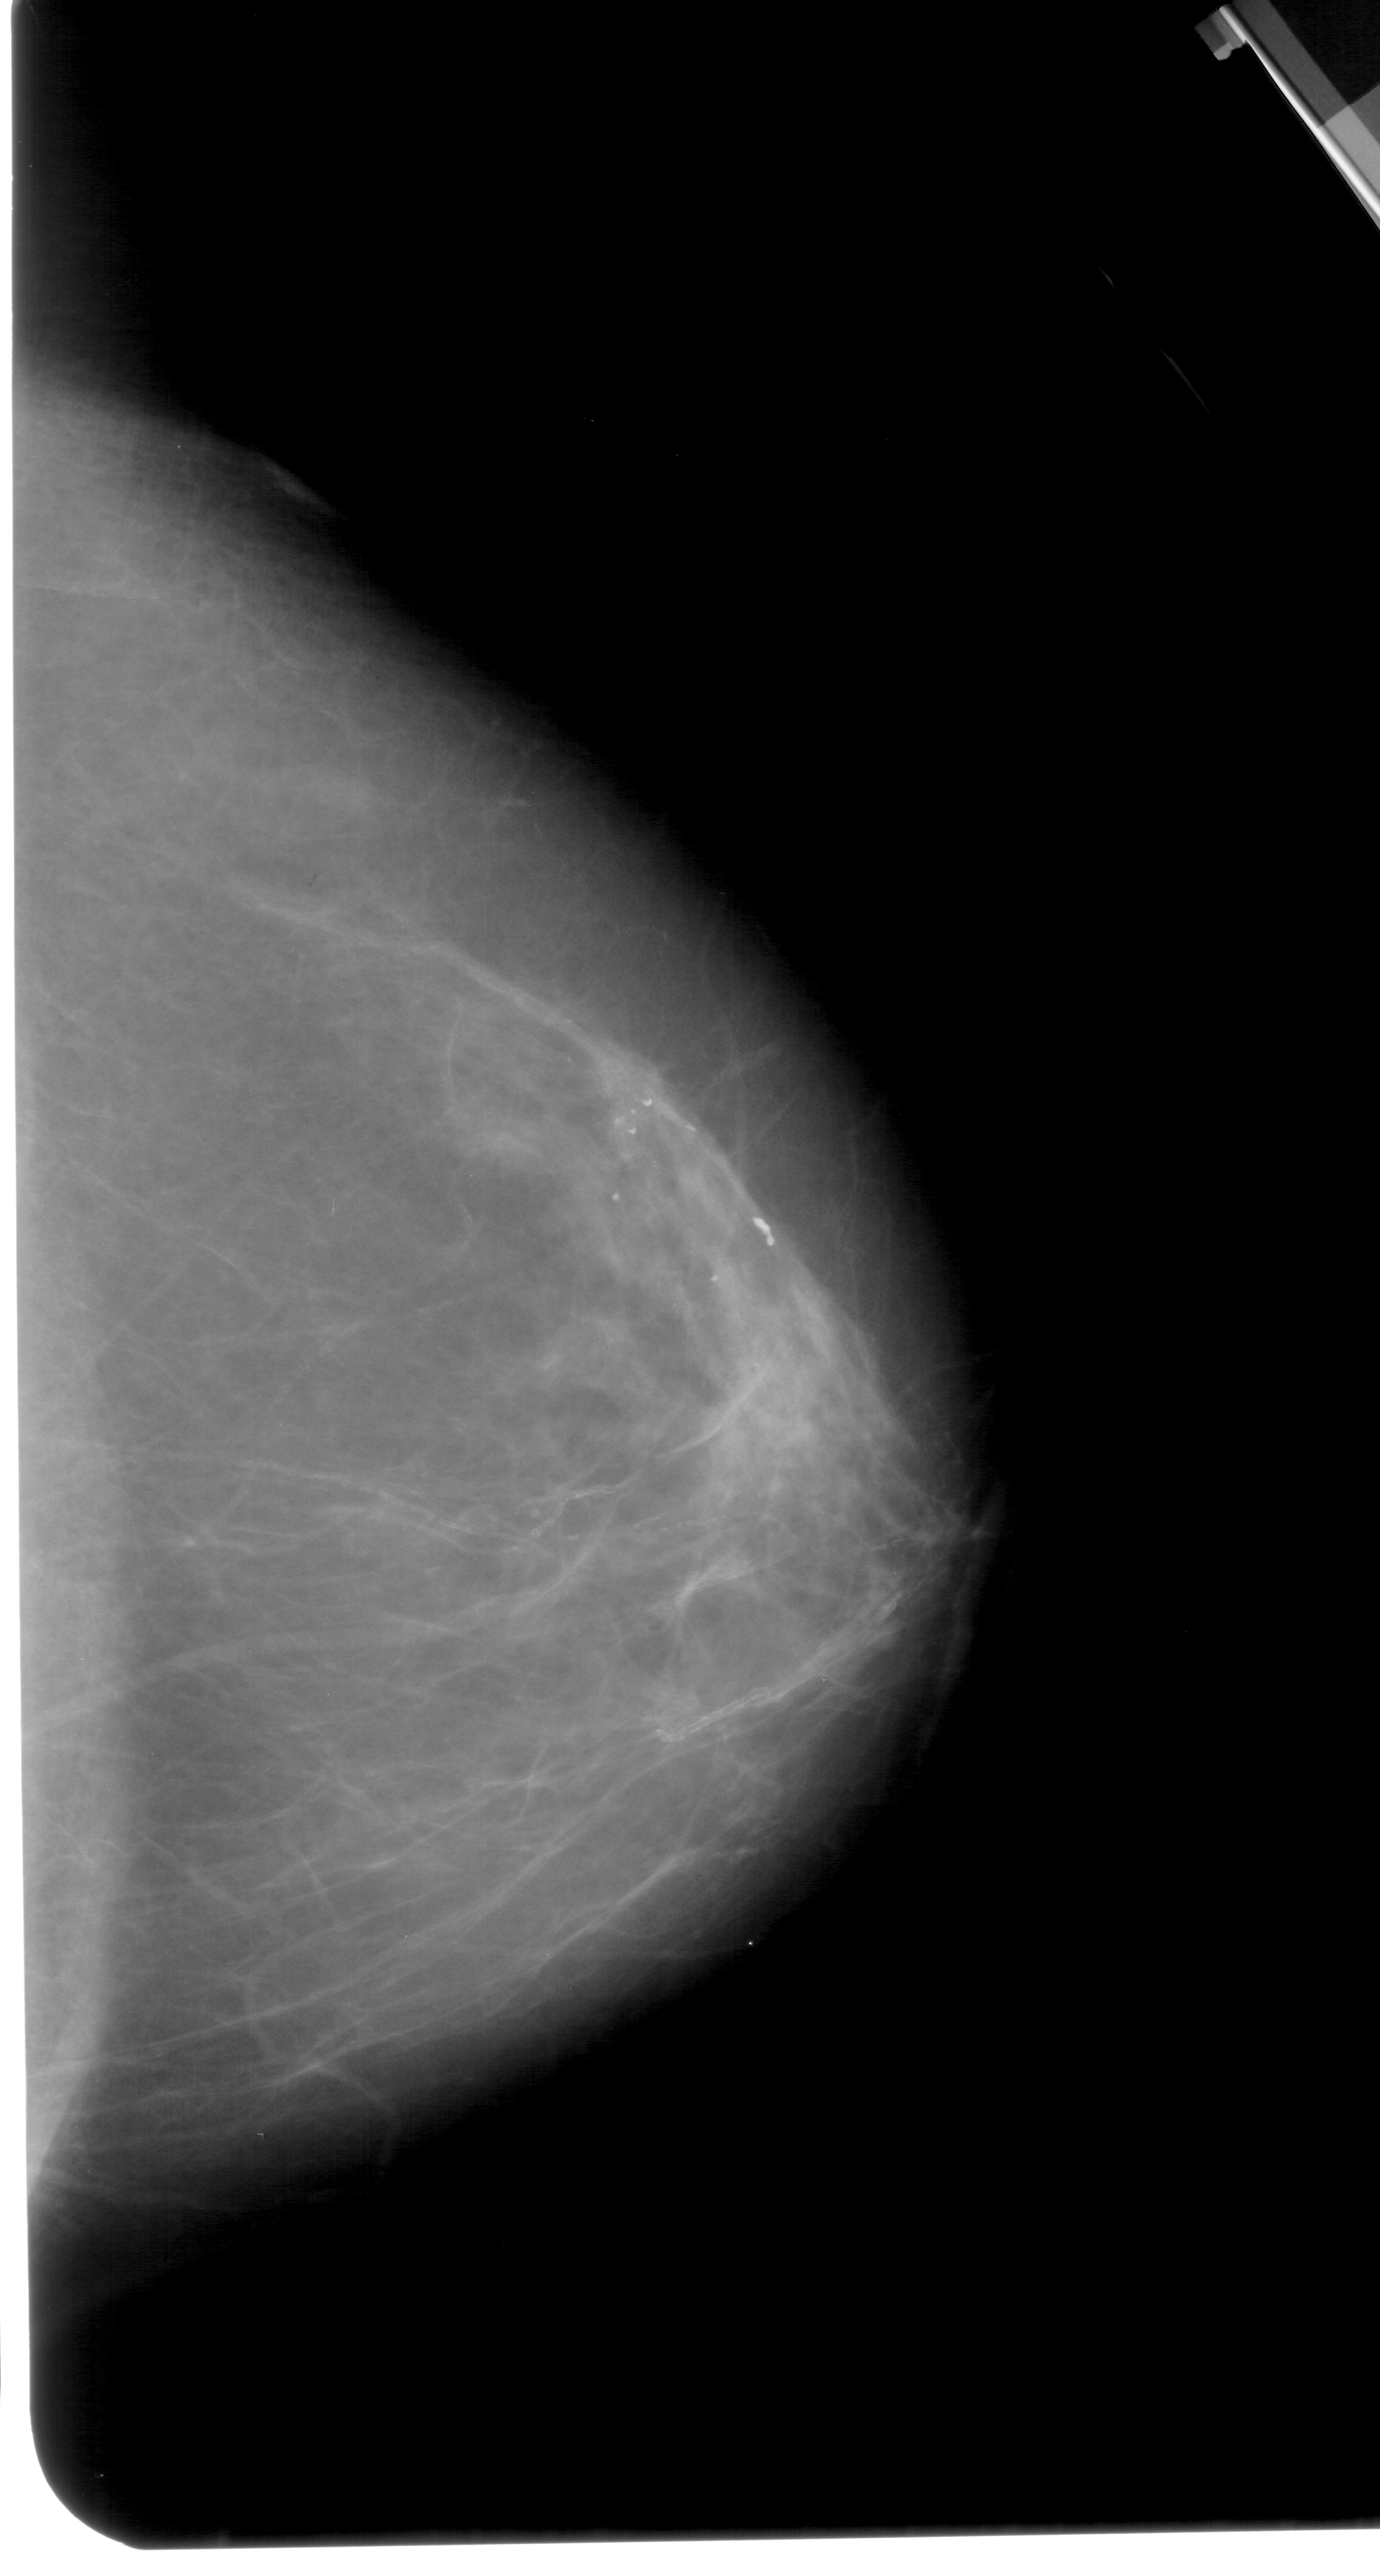
Mammogram (digitized film), right breast, CC view.
- Calcifications, morphology pleomorphic, distribution linear; BI-RADS assessment category 4; subtlety rating 2 on a 1 (subtle) to 5 (obvious) scale; pathology result (as recorded, not read from the image): malignant.